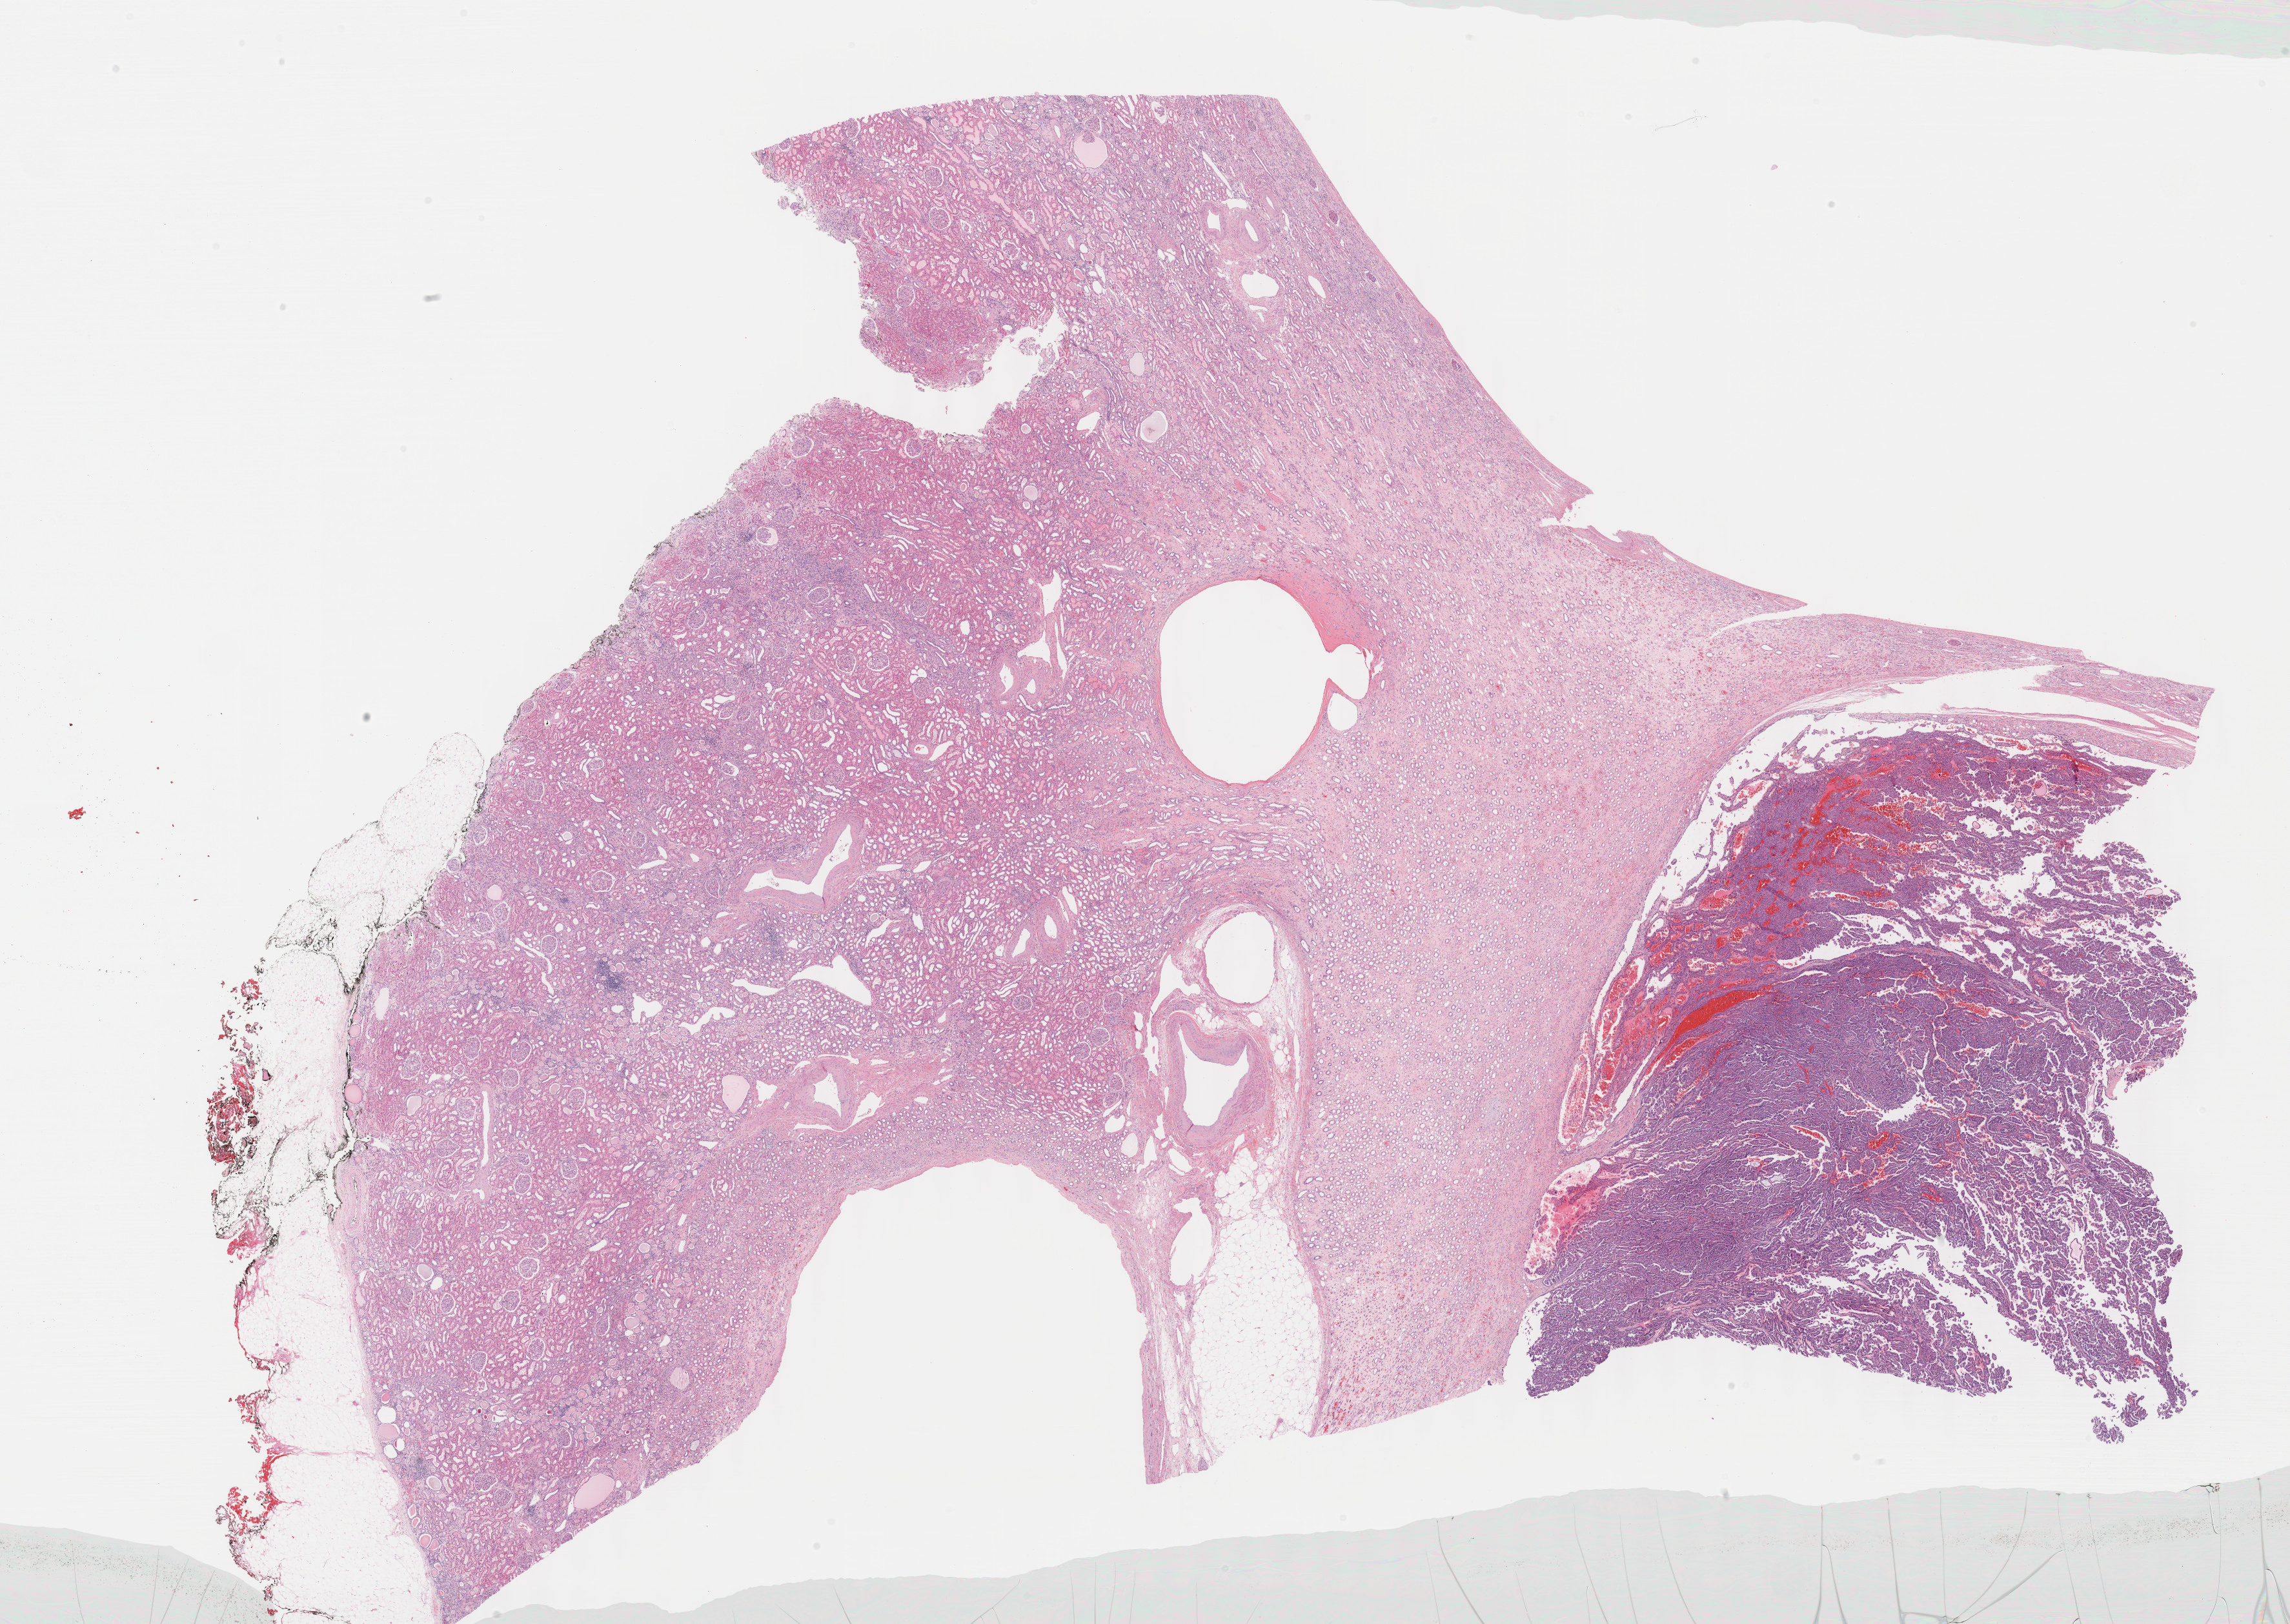
H&E-stained whole-slide image — whole scanned area (about 28.7 x 20.3 mm, slide scanned at 40x) shown as a low-resolution overview. Formalin-fixed paraffin-embedded (FFPE) diagnostic section. Primary tumour sample from the kidney. Male patient; age at initial diagnosis 65 years.
Diagnosis: Papillary adenocarcinoma, NOS.